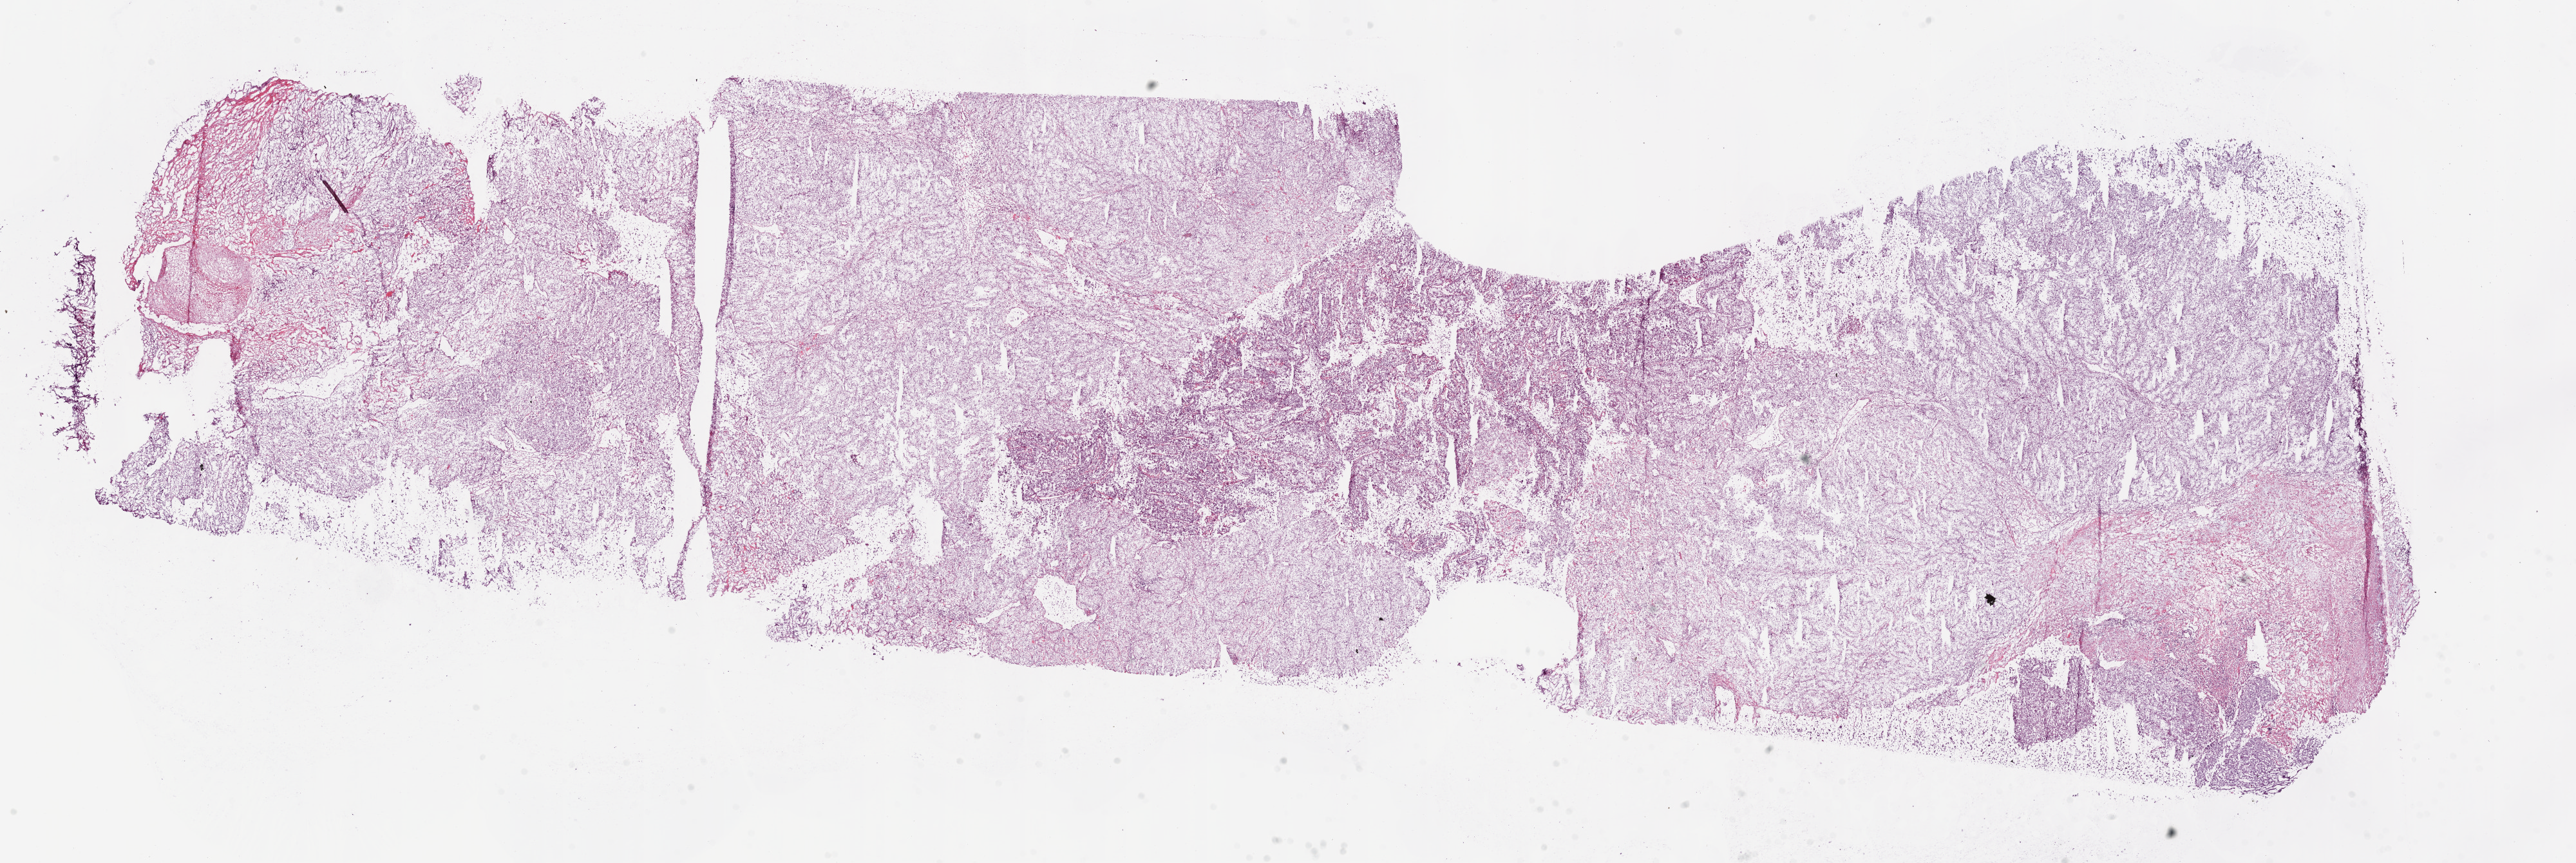
Whole-slide histology image, Hematoxylin and eosin (H&E) stained — low-resolution overview of the scanned area, about 32.1 x 10.8 mm (from a 20x scan); frozen section; primary tumour sample from the kidney. Patient: male, age at initial diagnosis 41 years. Histologic grade: G3 (poorly differentiated). Composition of this section per pathologist review: tumour cells 90%, tumour nuclei 85%, normal cells 0%, stromal cells 10%, necrosis 0%.
- histologic diagnosis: Clear cell adenocarcinoma, NOS
- laterality: right
- AJCC pathologic stage: III
- TNM: T3a NX M0